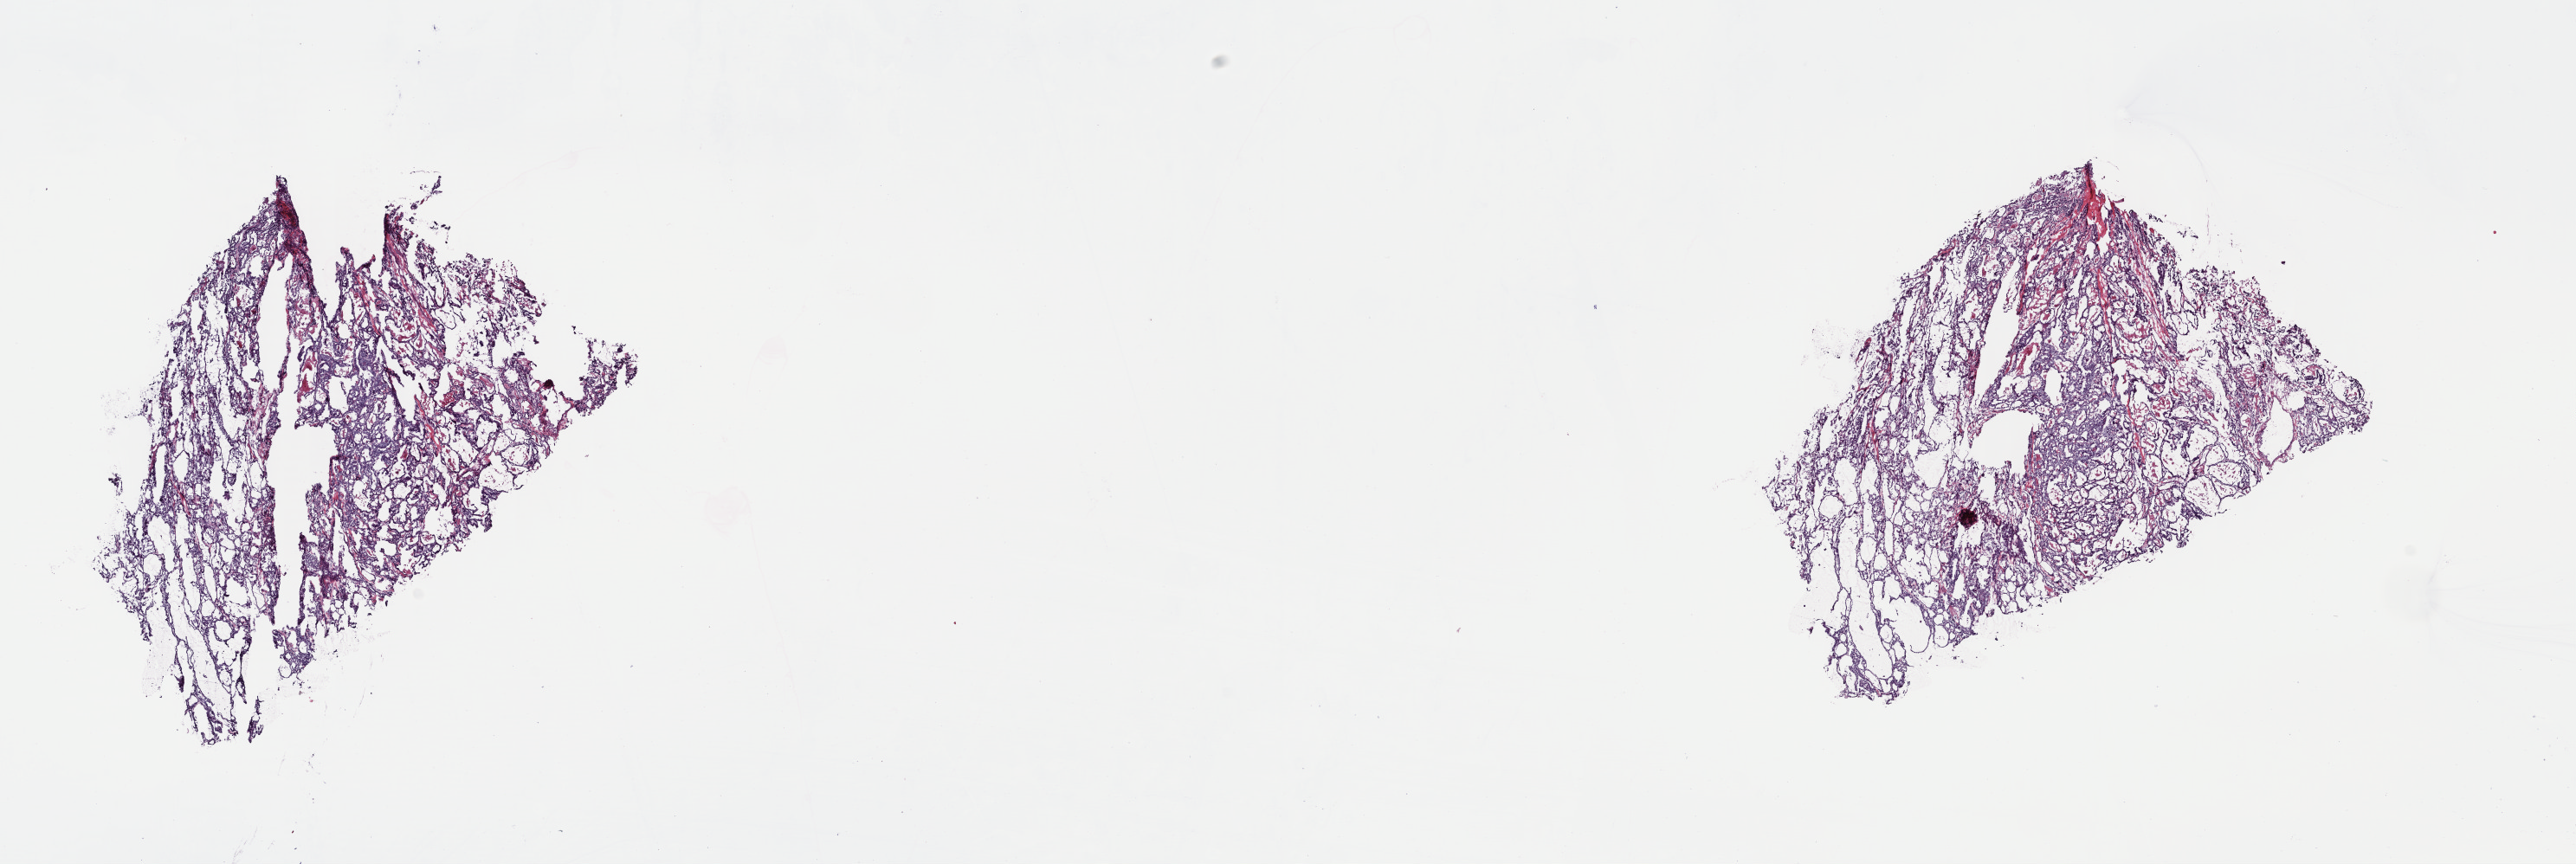
Digitized H&E-stained tissue section (whole slide) — a low-resolution overview of the entire scanned area, about 23.4 x 7.8 mm, frozen section from the top of the tissue portion, sample: primary tumour, thyroid. Female, age 68 years at initial diagnosis. Pathologist review of this section (percent, as recorded): tumour cells 90%, tumour nuclei 95%, normal cells 0%, stromal cells 10%, necrosis 0%. Inflammatory infiltration, as recorded: lymphocyte infiltration 0%, monocyte infiltration 0%, neutrophil infiltration 0%.
- diagnosis: Papillary adenocarcinoma, NOS (thyroid gland)
- lymph nodes positive (case pathology): 13 of 40 examined
- laterality: left
- AJCC pathologic stage: IVA